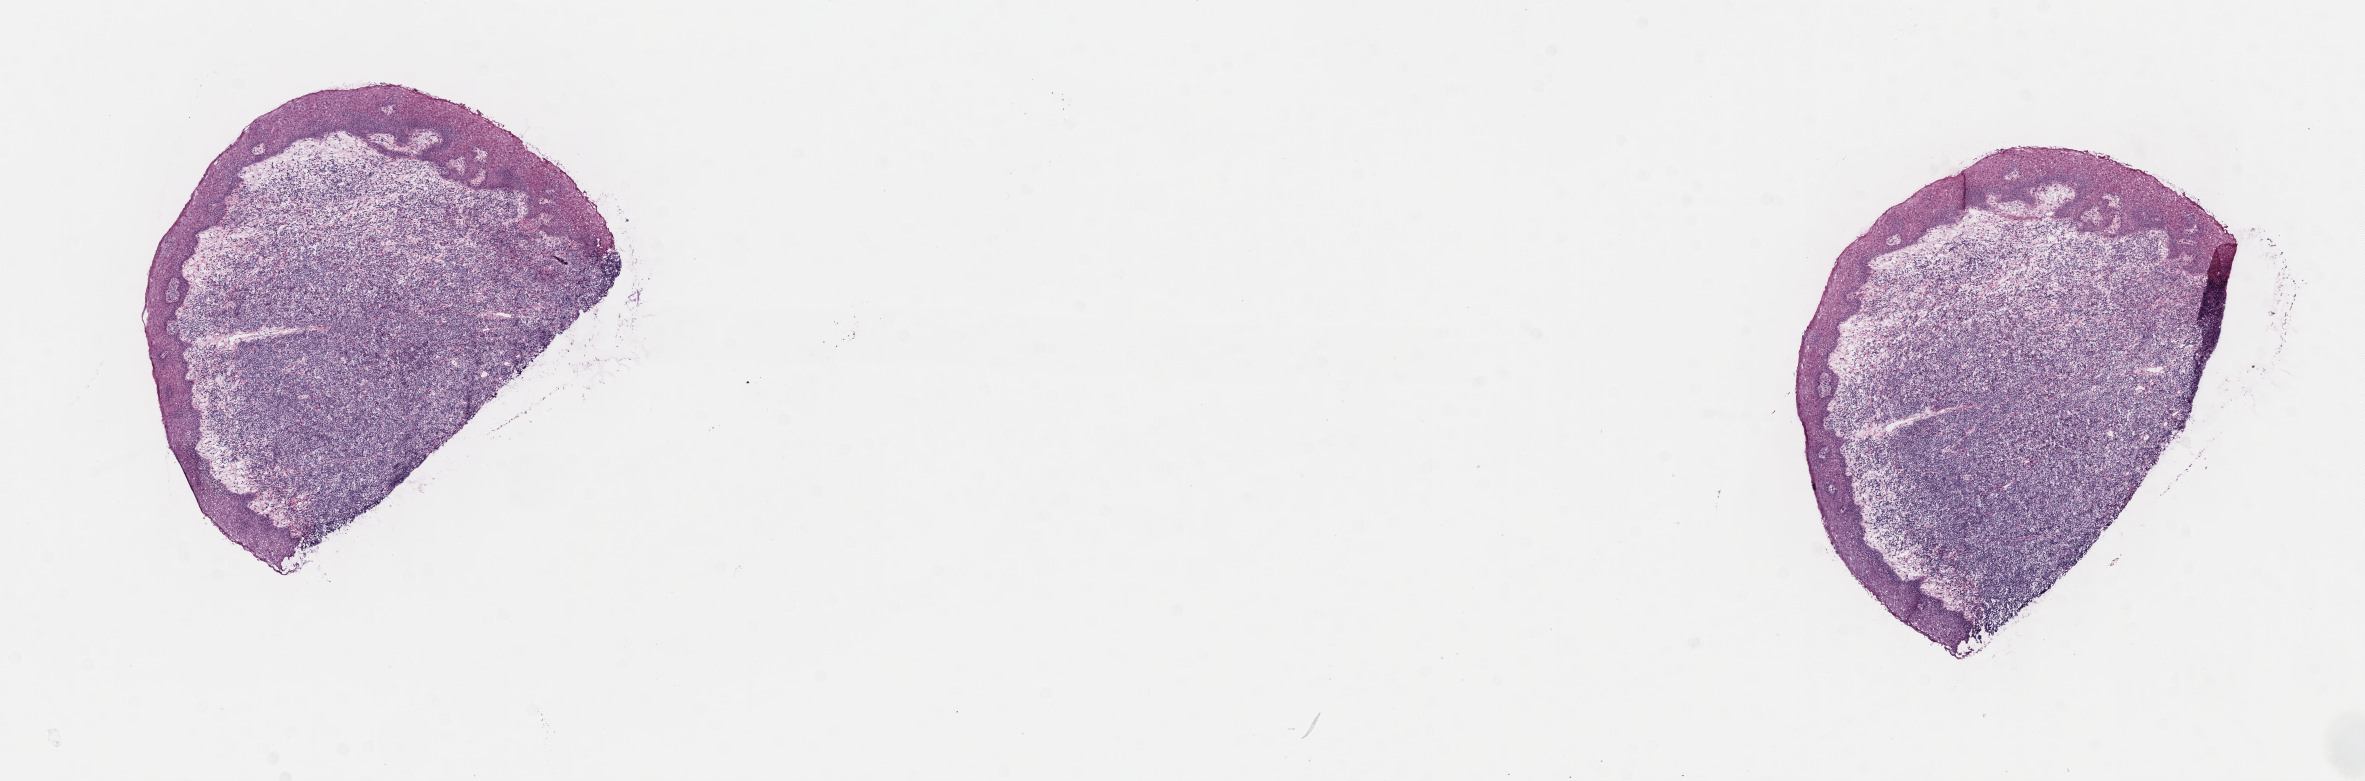
Digitized hematoxylin and eosin (H&E)-stained section, low-resolution overview of the scanned area, about 19.1 x 6.3 mm. Frozen section (tissue freezing medium). Specimen: primary tumor. Site: cranium. Patient: male, age at initial diagnosis 5 years. Slide review estimates, as recorded: tumor cells 65%, tumor nuclei 90%, stromal cells 5%, necrosis 30%, normal cells 0%. Infiltration values recorded for this section: lymphocyte infiltration 2%, monocyte infiltration 3%, neutrophil infiltration 0%.
- histologic diagnosis: Diffuse large B-cell lymphoma, NOS
- section: top of the tissue portion
- Ann Arbor stage (patient): Stage IV